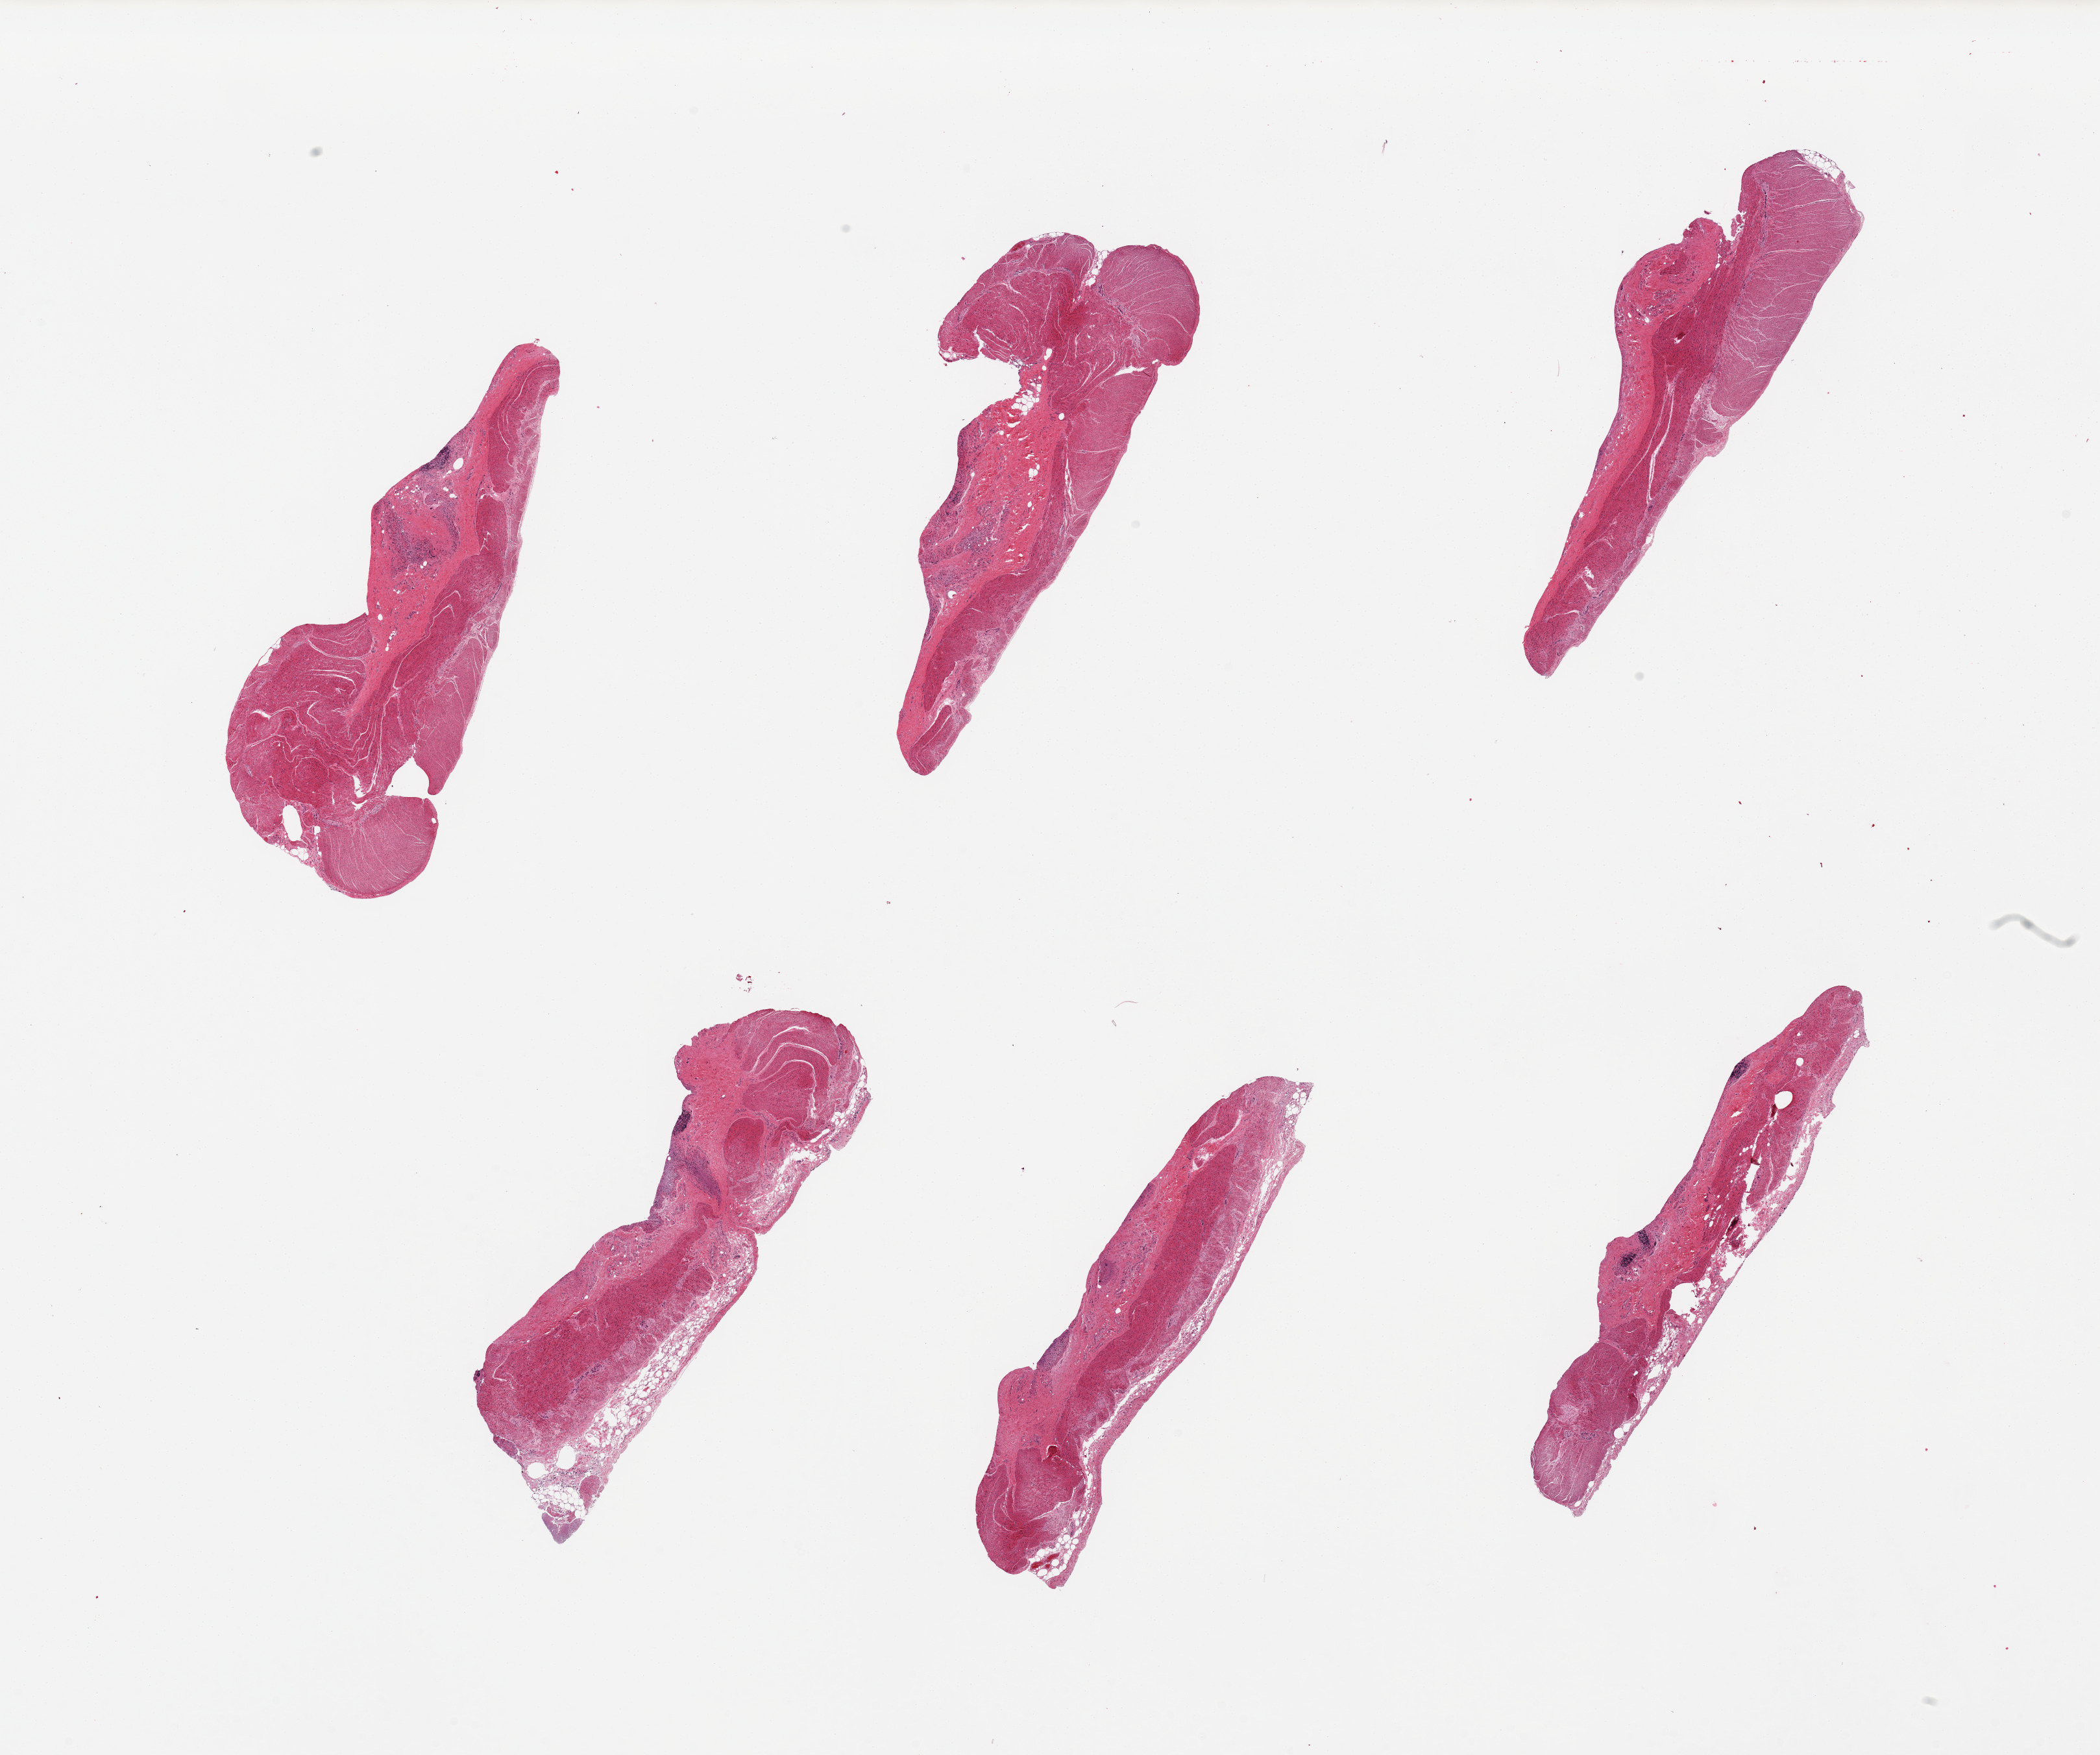
Haematoxylin and eosin whole-slide image, brightfield, whole scanned area (about 25.6 x 21.4 mm) shown as a low-resolution overview. PAXgene-fixed paraffin-embedded (PFPE) section. Sampled site (target tissue): sigmoid colon. Donor tissue sample.
Pathologist's review note for this sample: 6 pieces, ~10% adherent serosa, ~90% muscularis, unusually poorly preserved.